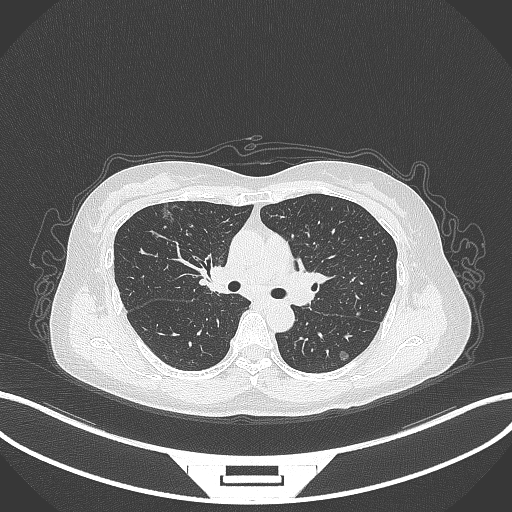
Chest CT, one axial slice; slice 202 of 315 in the series (ordered by position); 120 kVp; lung window (W 1500 / L -600 HU); 512 × 512 image matrix. Female patient, age 61 years. From the clinical record (not read from this slice): clinical TNM (as recorded): T1b N0 M0; histopathological grade: G1.
Annotated regions visible in this slice (rectangle marked by the reading radiologist):
- lung tumour (recorded histology: adenocarcinoma): bounding box [x1, y1, x2, y2] px = [157, 207, 174, 225]